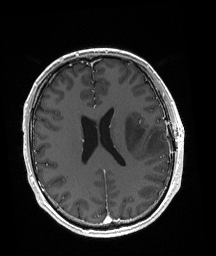
Brain MRI from a brain-tumour surgery series, one axial slice. Slice 79 of 192 in the series (ordered by position). T1-weighted post-contrast. 1 mm slice thickness. 216 × 256 image matrix, field of view 211 × 250 mm. From the clinical record (not read from this slice): histopathology: Astrocytoma; WHO grade: 3; IDH mutation: yes.
Annotated regions visible in this slice (manually delineated by an expert):
- tumour: box from (x=125, y=115) to (x=167, y=154) px